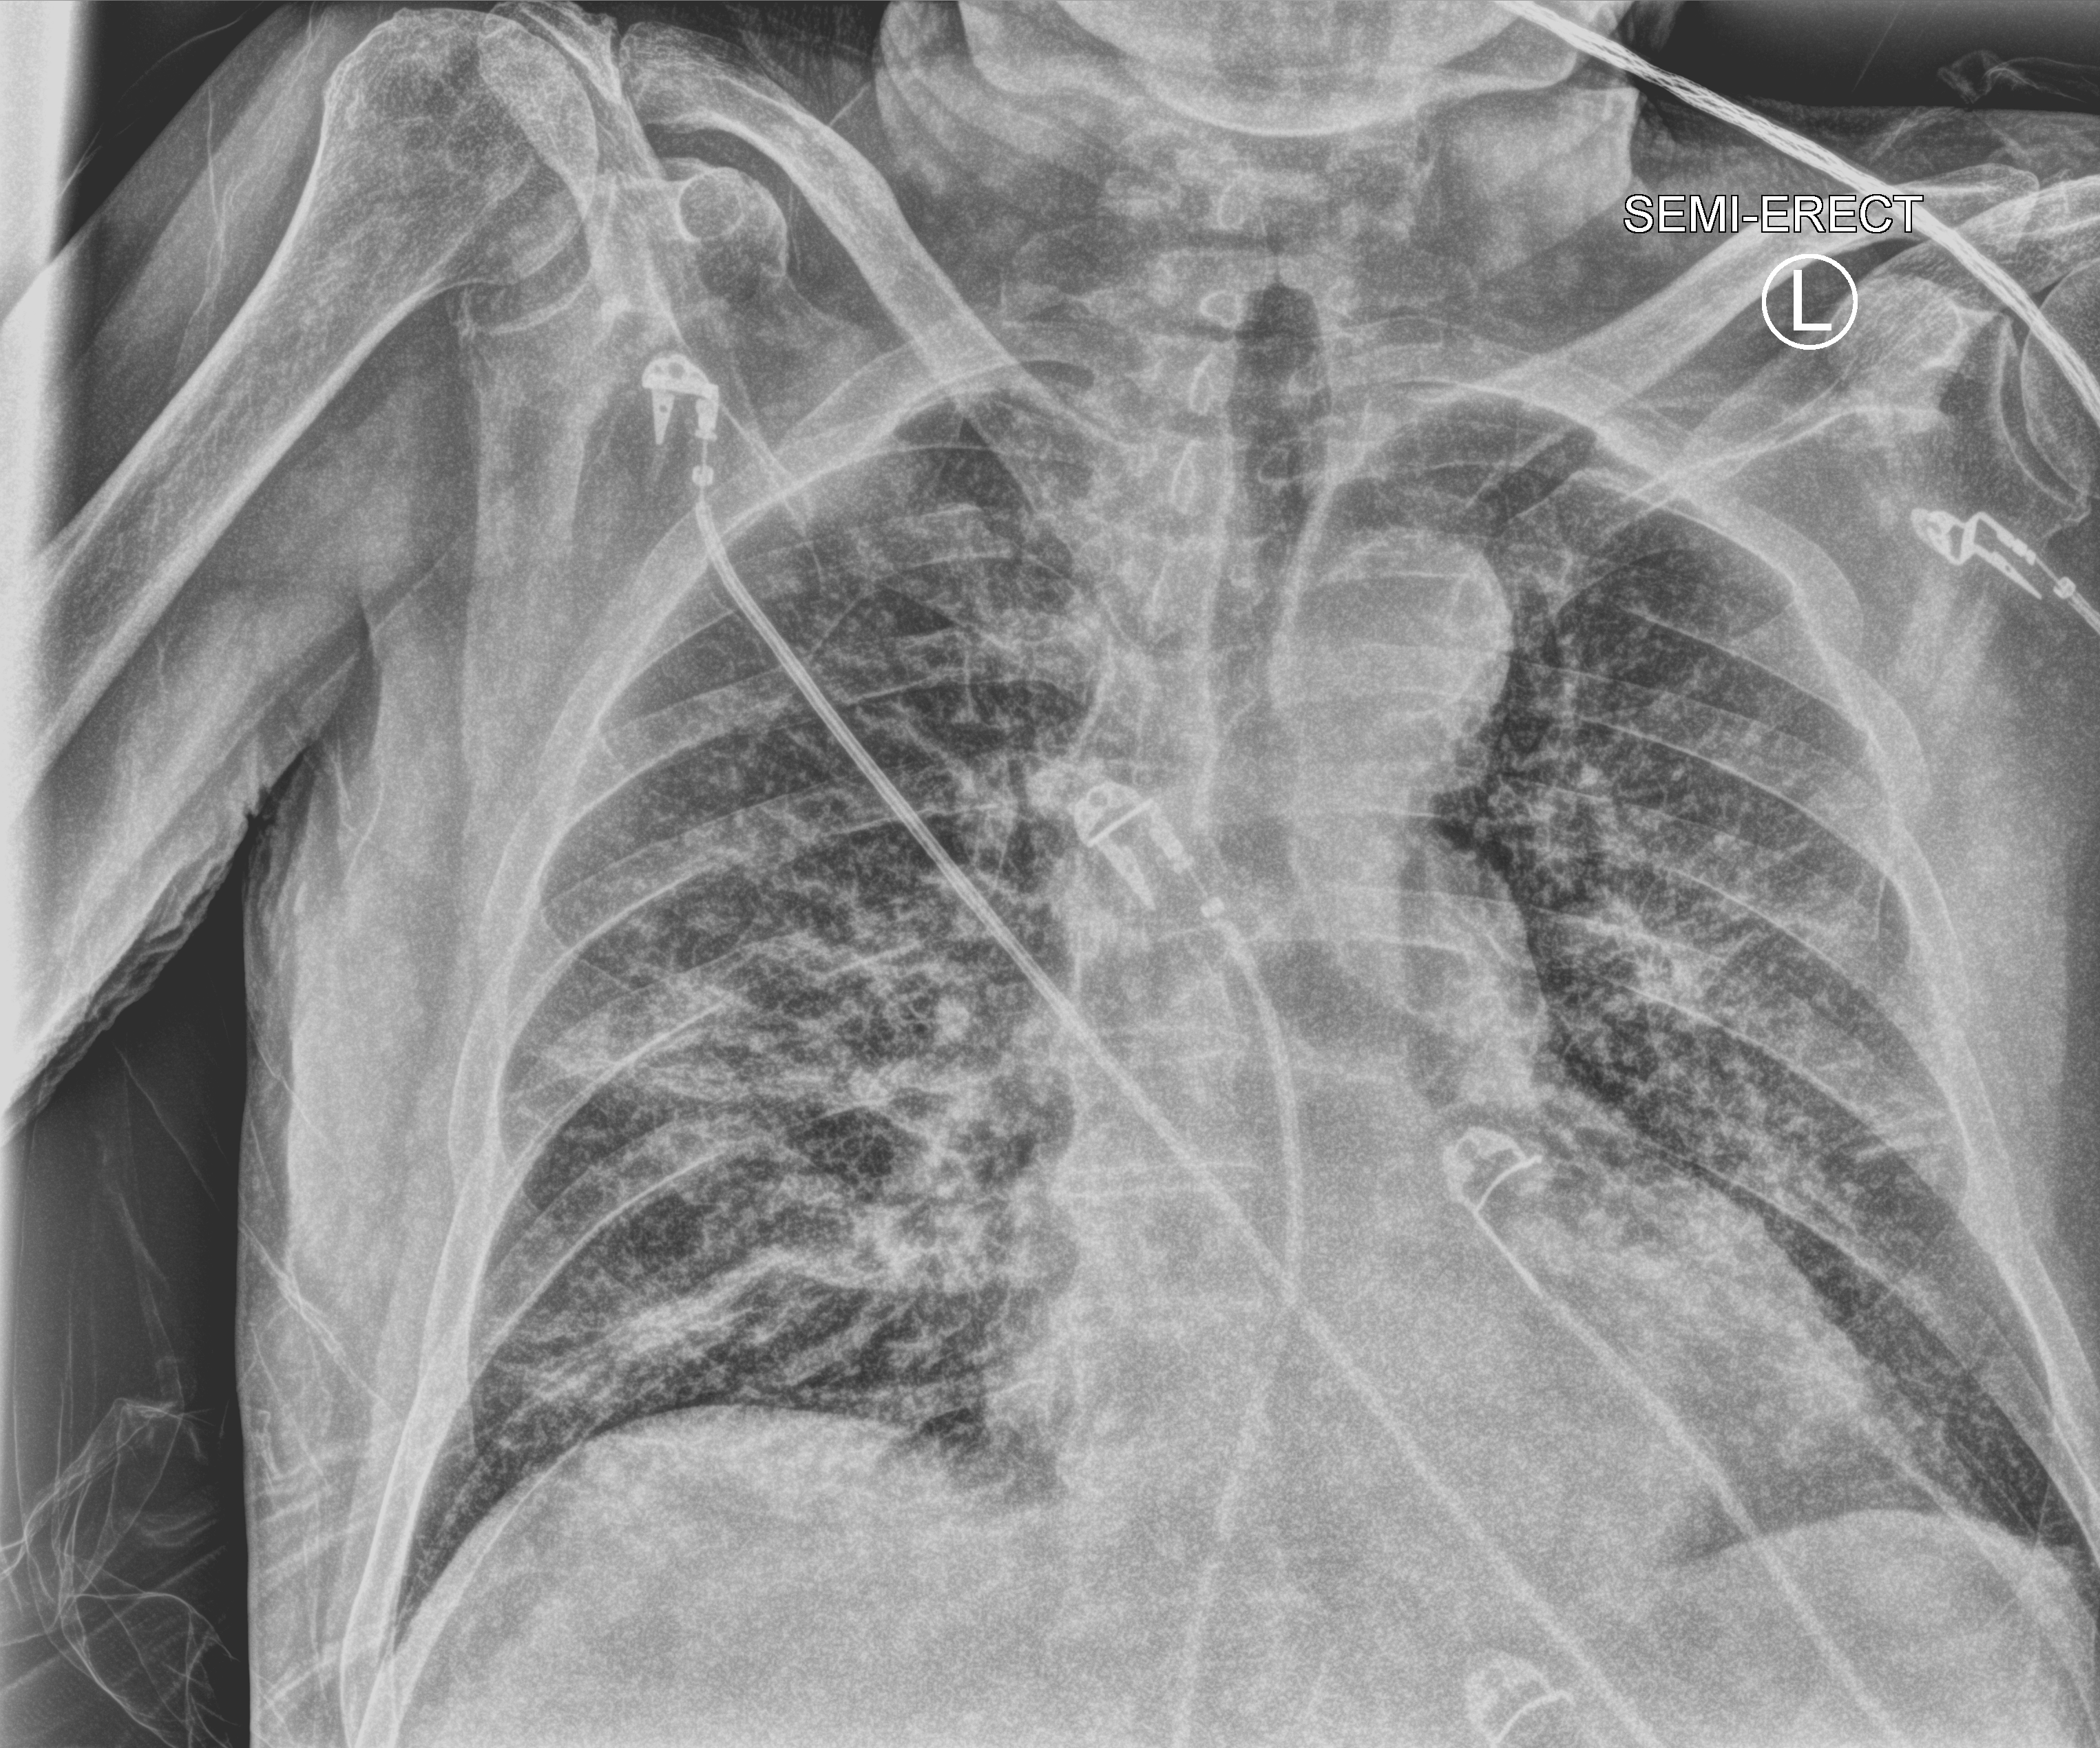
Chest X-ray (portable); anteroposterior (AP) projection. Patient hospitalised with COVID-19; male, aged 75–90 years.
Hospital-stay facts (about this admission, not read from this image; timing relative to this image not recorded):
- mechanically ventilated during this hospital stay: yes